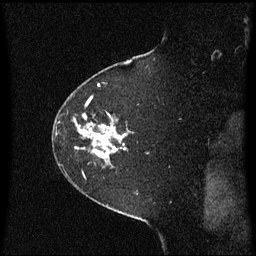
Breast MRI (dynamic contrast-enhanced), one sagittal slice; position 50 of 60 along the scan axis; dynamic contrast-enhanced series, image 2 of 3 at this slice position (ordered by acquisition); 1.5 T; TE 4.2 ms, TR 8.4 ms; 2 mm slice thickness; 256 × 256 image matrix, field of view 210 × 210 mm. Female patient, age 60 years. Case-level facts recorded for this patient, not image findings: setting: breast cancer imaged before/during neoadjuvant chemotherapy; receptor status: triple-negative.
Annotated regions visible in this slice (semi-automatic segmentation, software-assisted and operator-edited):
- analysis volume of interest (the breast-tissue region the enhancement analysis was run in; not a lesion): bounding box <54,99,136,177> (left, top, right, bottom; pixels)
- tumour enhancement mask (voxels above the 70 % enhancement threshold inside the analysis volume of interest): <80,128,123,157>